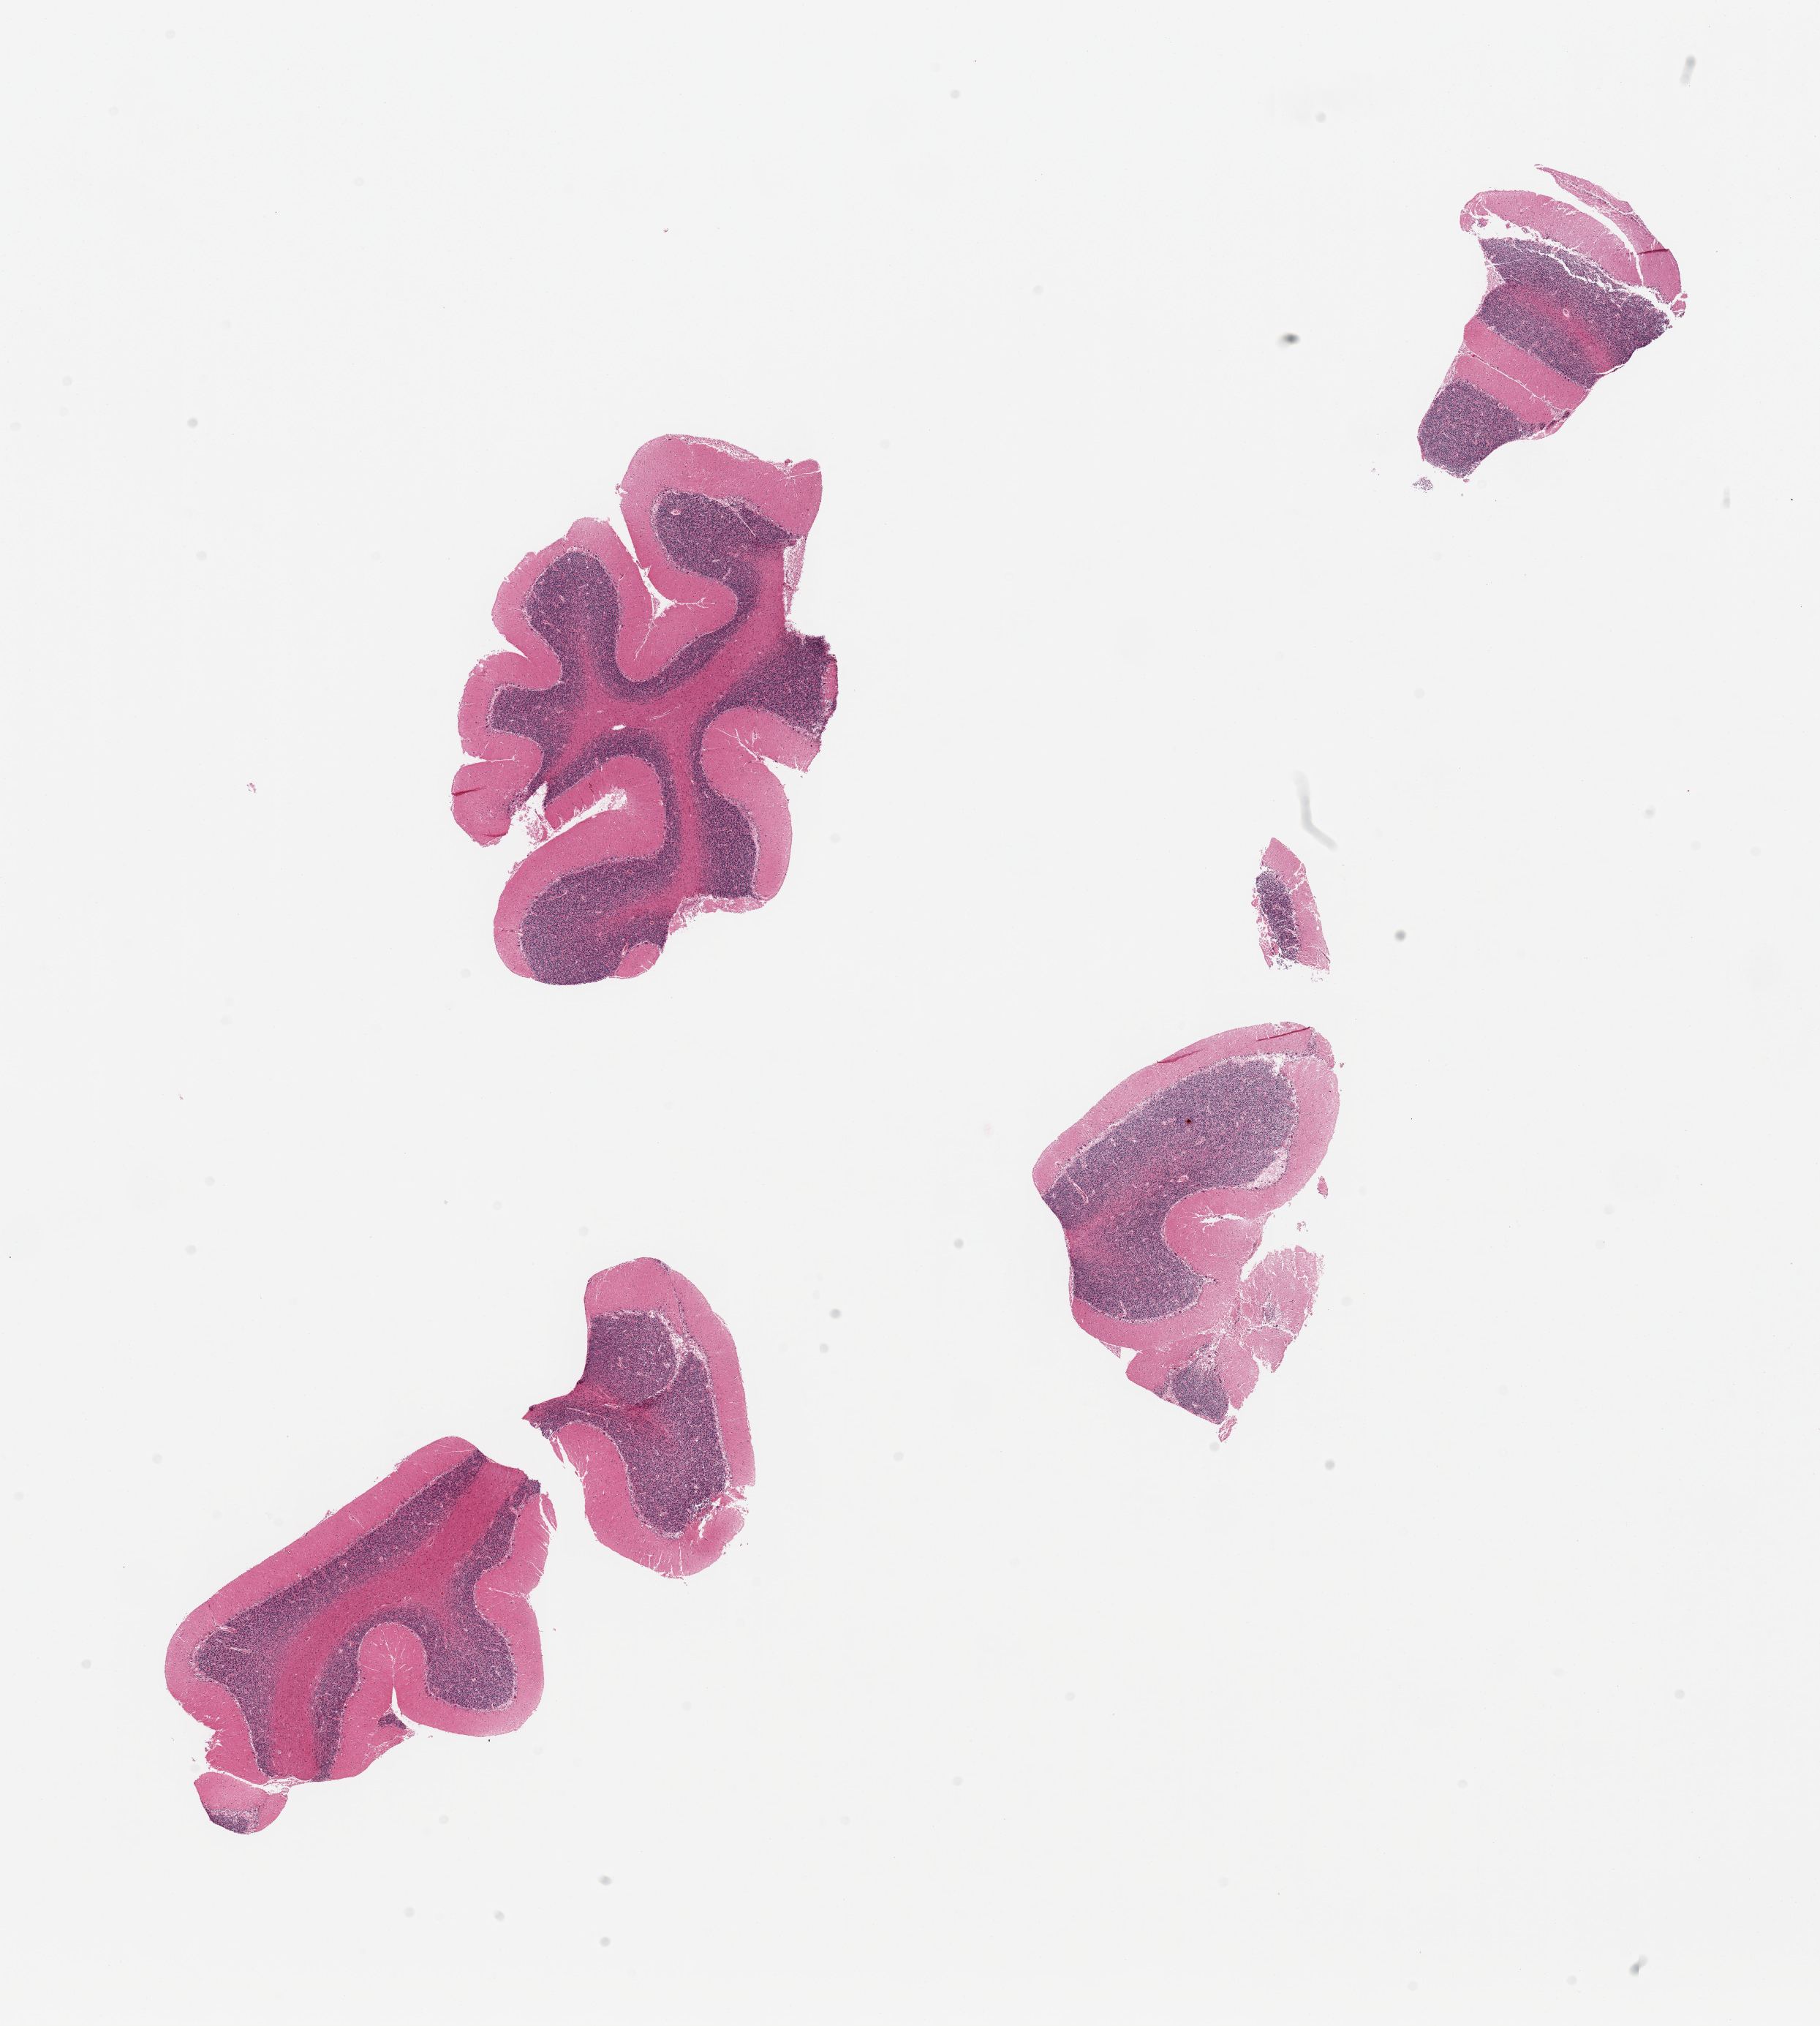
Digitized haematoxylin and eosin-stained section, brightfield — a low-resolution overview of the entire scanned area, about 19.7 x 21.9 mm. PAXgene-fixed paraffin-embedded (PFPE) section. Target tissue: cerebellum. Donor tissue sample. Donor: male.
Pathologist's review note for this sample: 4 pieces (fragmented); Purkinje cells visualized.